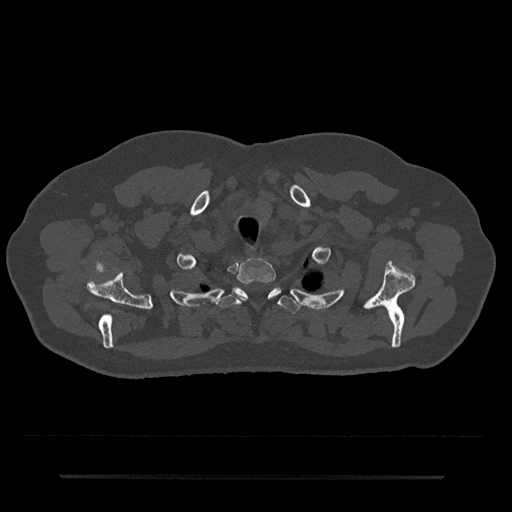
CT including the spine, one axial slice. Position 621 of 797 along the scan axis. Reconstruction kernel Br40s/3. Bone window (W 1800 / L 400 HU). 512 × 512 image matrix. Male patient, age 69 years. From the clinical record (not read from this slice): primary cancer: prostate.
Structures marked on this image (semi-automatic segmentation, software-assisted and operator-edited):
- T1 vertebra: box from (x=237, y=258) to (x=276, y=284) px
- T2 vertebra: (x=218, y=287)–(x=300, y=313)